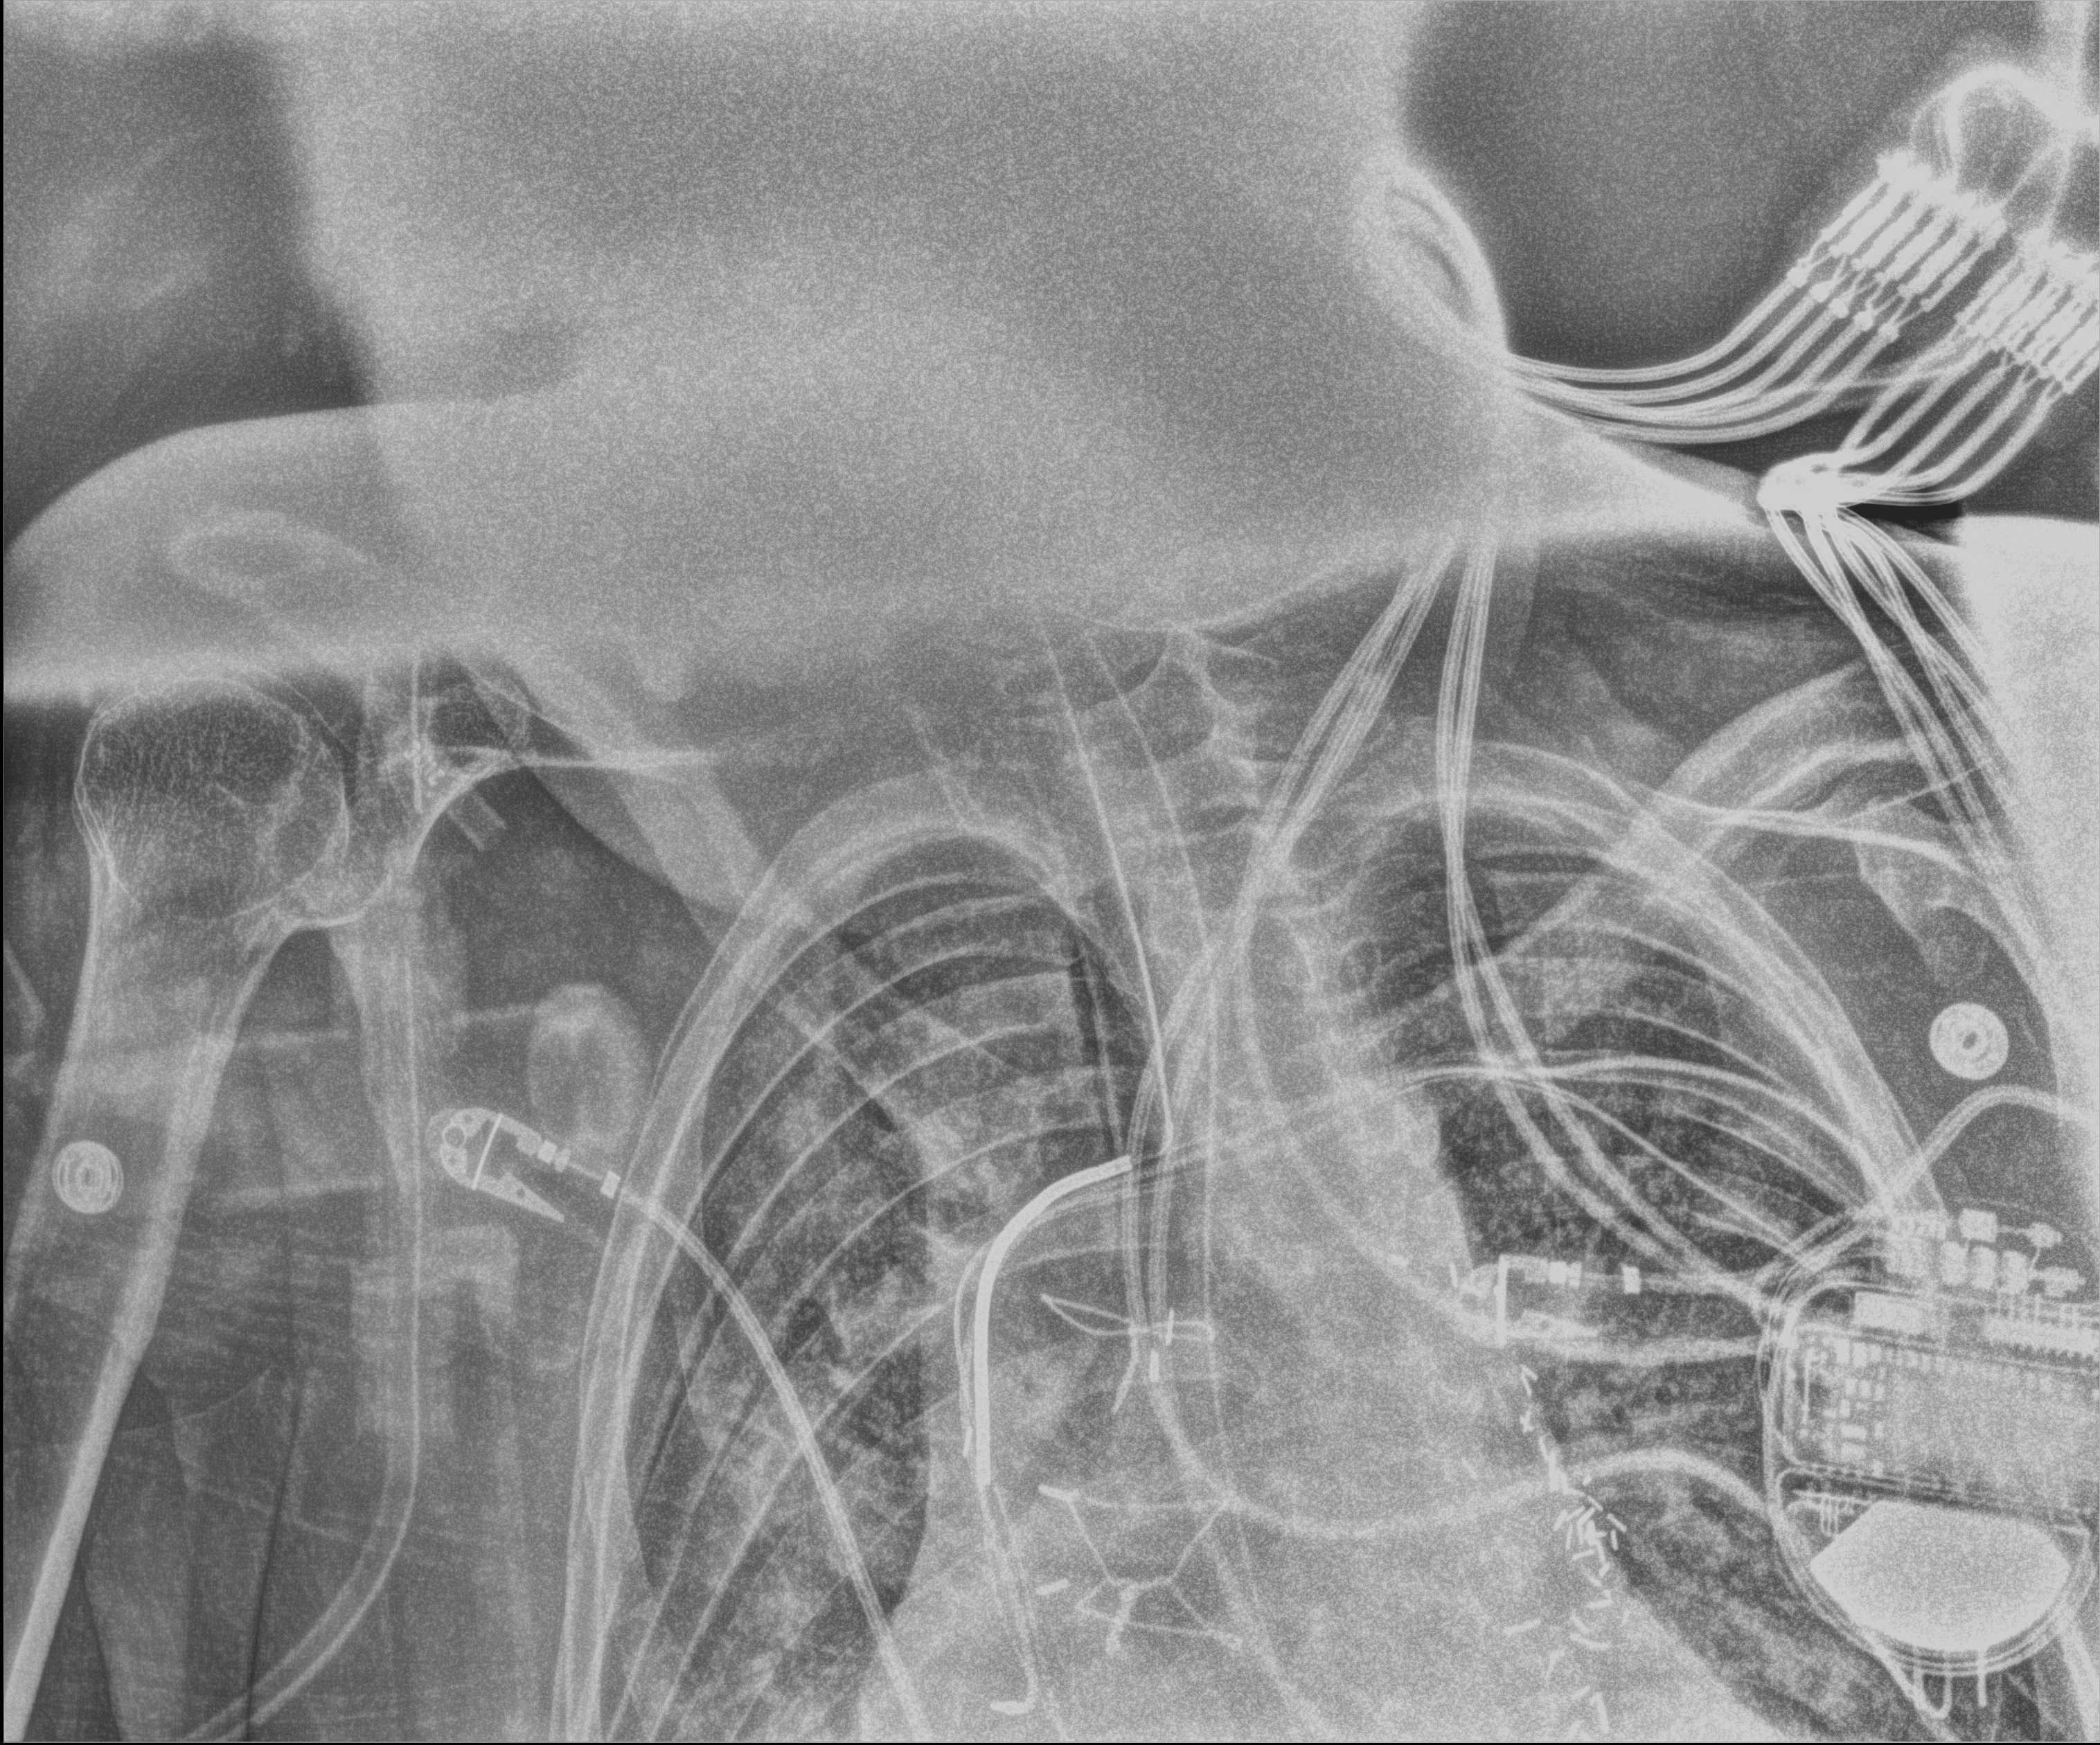
Bedside chest radiograph (digital radiography), anteroposterior (AP) projection. Male patient hospitalised with COVID-19, age 60–74 years.
From the hospital-stay record, not from the radiograph (when in the stay this image was taken is not recorded): mechanically ventilated during this hospital stay: yes.